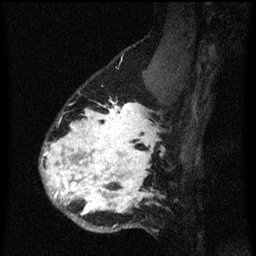
Breast MRI (dynamic contrast-enhanced), one sagittal slice. Position 46 of 60 along the scan axis. Dynamic contrast-enhanced series, image 2 of 3 at this slice position (ordered by acquisition). 1.5 T. TE 4.2 ms, TR 8.4 ms. 2 mm slice thickness. 256 × 256 image matrix, field of view 180 × 180 mm. Patient: female, 34 years. From the clinical record (not read from this slice): setting: breast cancer imaged before/during neoadjuvant chemotherapy; receptor status: HR-positive, HER2-negative.
Outlined on this slice (semi-automatic segmentation, software-assisted and operator-edited):
- analysis volume of interest (the breast-tissue region the enhancement analysis was run in; not a lesion): bounding box (x1, y1, x2, y2) in pixels: (40, 58, 173, 233)
- tumour enhancement mask (voxels above the 70 % enhancement threshold inside the analysis volume of interest): (42, 102, 157, 215)